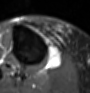
MRI of an extremity soft-tissue mass, one axial slice; position 39 of 60 along the scan axis; STIR; MR volume resampled by the dataset authors to the PET/CT grid (not the native acquisition matrix); 3.27 mm slice thickness; 90 × 93 image matrix, field of view 88 × 91 mm. Female patient. From the clinical record (not read from this slice): histological type: undifferentiated – high grade; grade: high; site of the primary tumour: right thigh.
Structures marked on this image (expert contour drawn on MRI and transferred to this co-registered scan by the dataset authors):
- gross tumour volume (mass): bounding box [x1, y1, x2, y2] px = [46, 47, 61, 70]